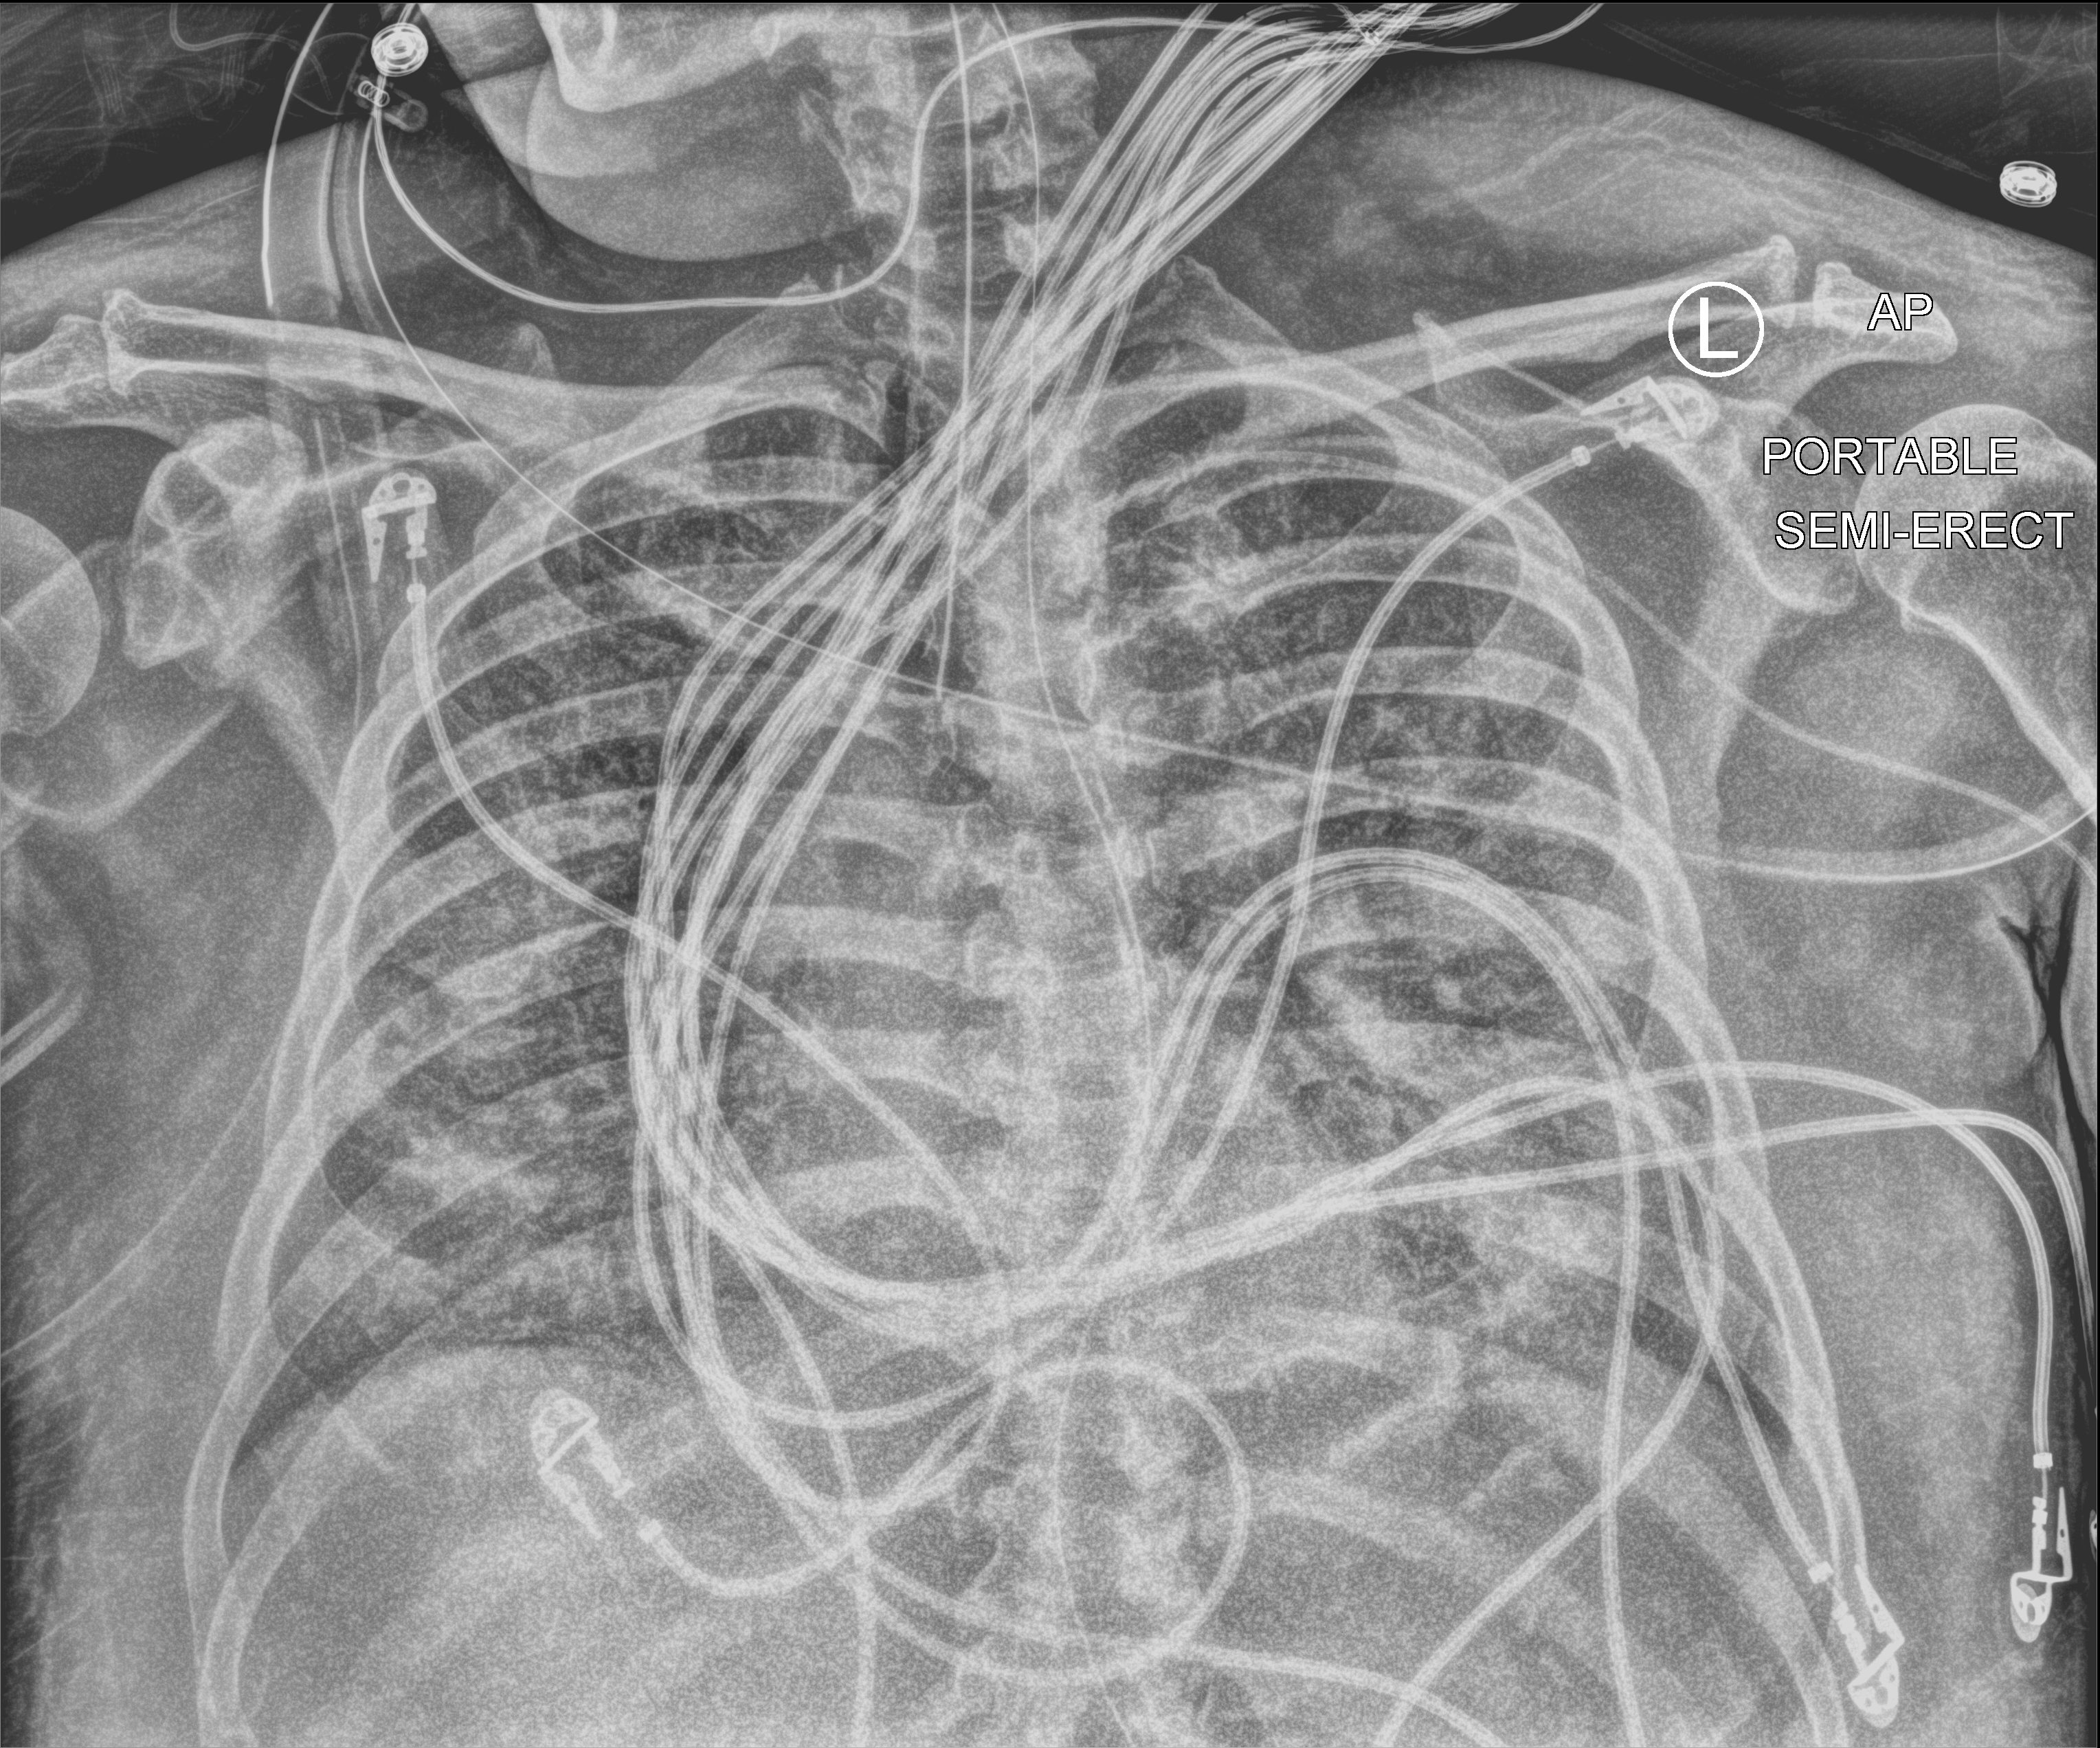
Bedside chest radiograph (computed radiography), anteroposterior (AP) projection. Male patient hospitalised with COVID-19, age 60–74 years.
Hospital-stay facts (about this admission, not read from this image; timing relative to this image not recorded):
- COPD (admission record): no
- admitted to intensive care during this hospital stay: yes